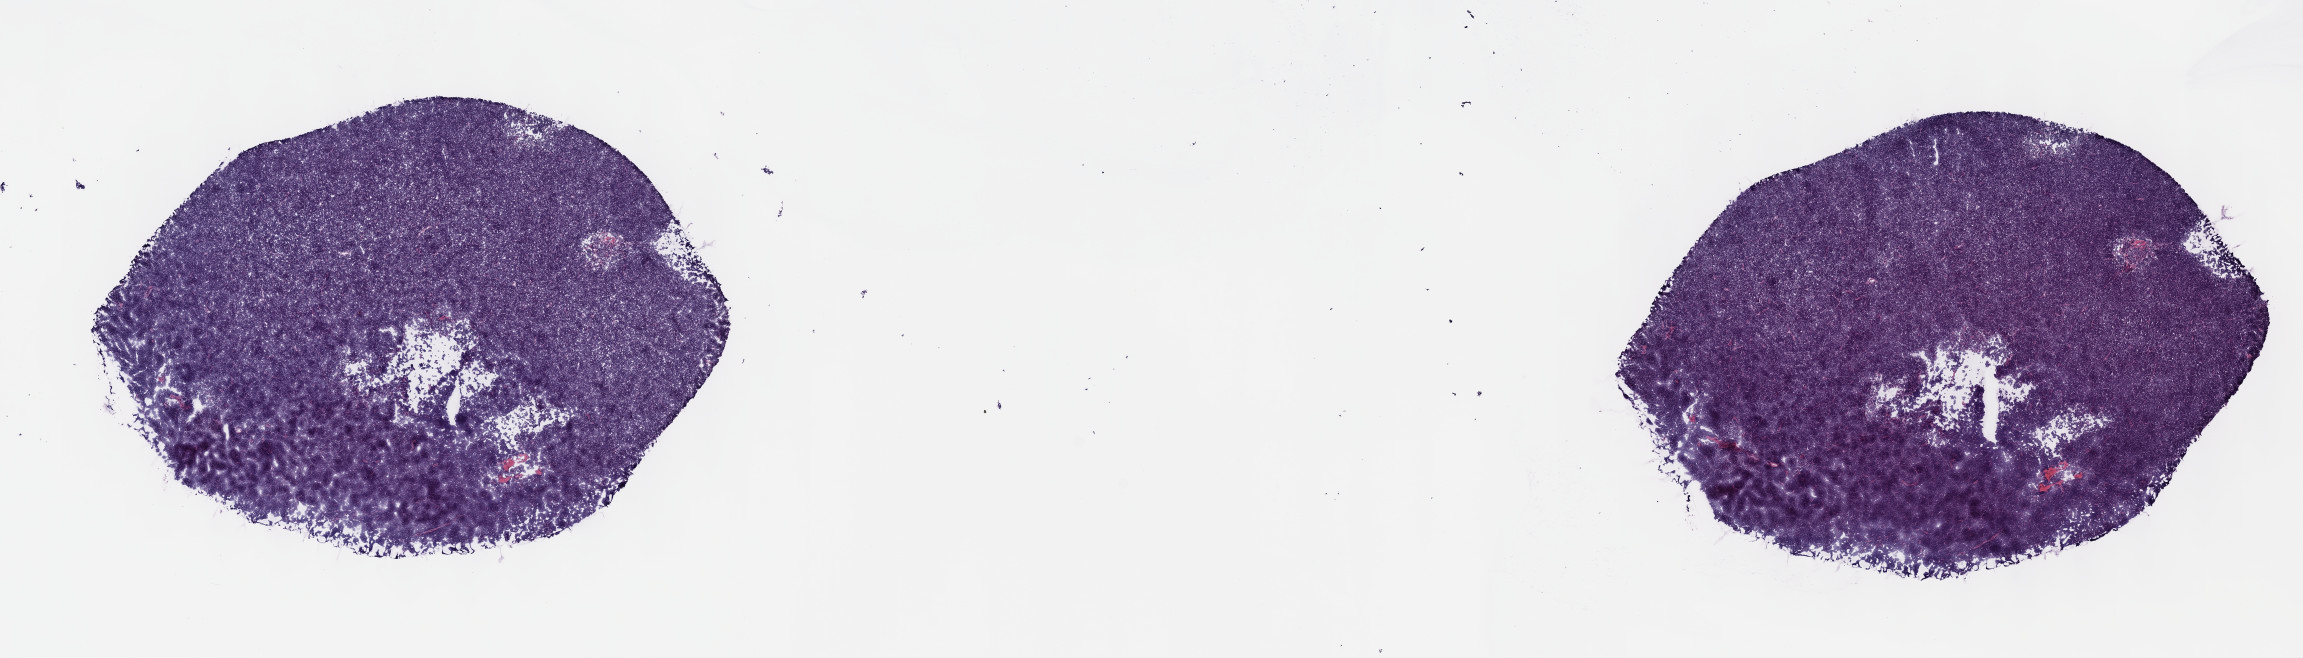
H&E whole-slide image, low-resolution overview of the scanned area, about 18.6 x 5.3 mm, frozen section, thymus, primary tumour sample. Female, age 79 years at initial diagnosis.
Histologic diagnosis: Thymoma, type B1, malignant.